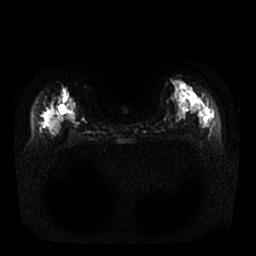
Breast MRI, one axial slice; slice 12 of 25 in the series (ordered by position); diffusion-weighted series; image 2 of 4 stored at this slice position (different b-values; order by instance number); 1.5 T; 256 × 256 image matrix, field of view 340 × 340 mm. Female patient.
Outlined on this slice (expert manual segmentation):
- tumour on diffusion-weighted imaging: bounding box [x1, y1, x2, y2] px = [45, 114, 55, 126]